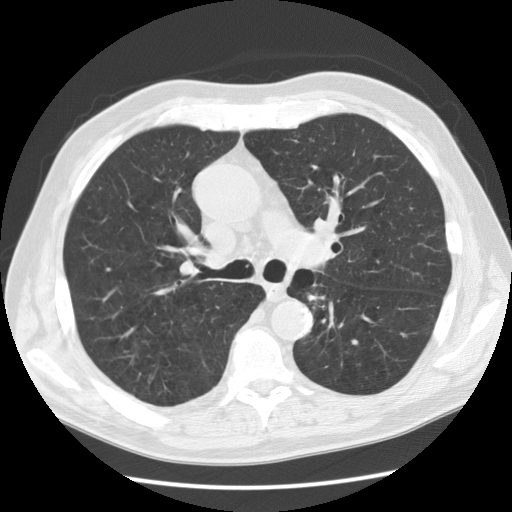
Low-dose screening chest CT, one axial slice; slice 82 of 130 in the series (ordered by position); reconstruction kernel STANDARD; 120 kVp; lung window (W 1500 / L -600 HU); 512 × 512 image matrix.
Outlined on this slice (outlined manually by an expert reader):
- lesion 1 (tumor, lower lobe of left lung): box from (x=308, y=287) to (x=326, y=308) px